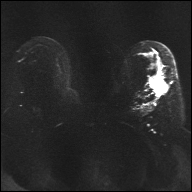
Breast MRI, one axial slice. Slice 21 of 32 in the series (ordered by position). Diffusion-weighted series; image 2 of 4 stored at this slice position (different b-values; order by instance number). 1.5 T. 4 mm slice thickness. 192 × 192 image matrix, field of view 360 × 360 mm. Female patient.
Outlined on this slice (manually delineated by an expert):
- tumour on diffusion-weighted imaging: bounding box [x1, y1, x2, y2] px = [149, 76, 167, 96]